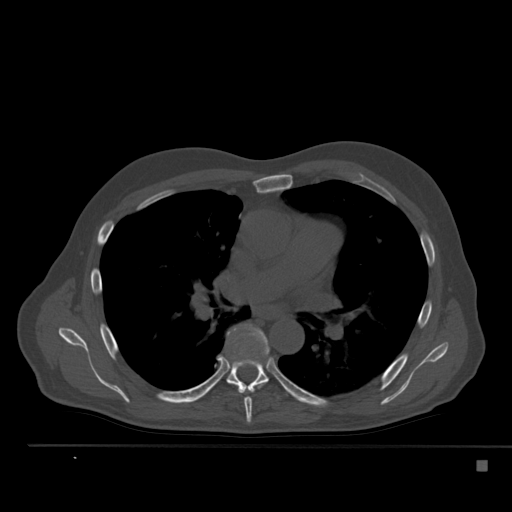
CT including the spine, one axial slice; position 337 of 517 along the scan axis; reconstruction kernel Br40s; 120 kVp; bone window (W 1800 / L 400 HU); 1.5 mm slice thickness; 512 × 512 image matrix, field of view 408 × 408 mm. Male patient, age 70 years. Case-level facts recorded for this patient, not image findings: primary cancer: renal; vertebrae with lytic lesions (as recorded): T4, T6, T10, T12, L3, L4, L5.
Outlined on this slice (semi-automatic segmentation, software-assisted and operator-edited):
- T6 vertebra: bounding box <244,325,269,423> (left, top, right, bottom; pixels)
- T7 vertebra: <203,360,291,398>